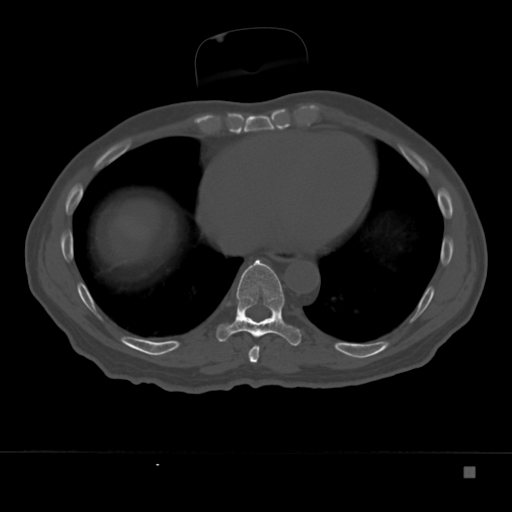
CT including the spine, one axial slice; position 191 of 332 along the scan axis; 120 kVp; bone window (W 1800 / L 400 HU); 1.5 mm slice thickness; 512 × 512 image matrix. Male patient, age 72 years. Case-level facts recorded for this patient, not image findings: primary cancer: skeletal.
Annotated regions visible in this slice (semi-automatically segmented with operator editing):
- T8 vertebra: box from (x=248, y=345) to (x=260, y=363) px
- T9 vertebra: (x=216, y=259)–(x=301, y=346)